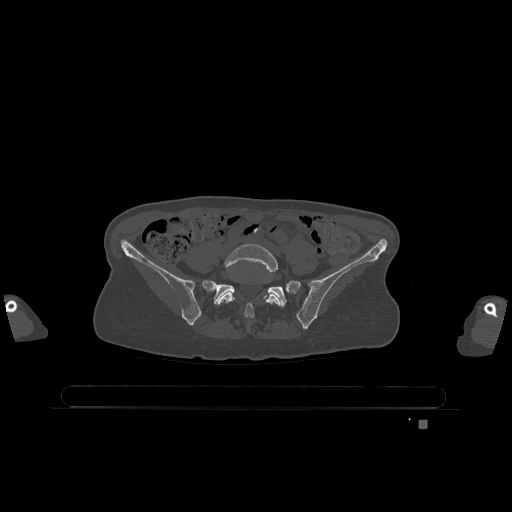
CT including the spine, one axial slice; slice 218 of 1317 in the series (ordered by position); bone window (W 1800 / L 400 HU); 512 × 512 image matrix, field of view 500 × 500 mm. Patient: female, 74 years. From the clinical record (not read from this slice): primary cancer: lung; vertebrae with lytic lesions (as recorded): T1, T4, T5, T6, L4, L5.
Outlined on this slice (semi-automatic segmentation, software-assisted and operator-edited):
- L5 vertebra: bounding box [x1, y1, x2, y2] px = [217, 244, 281, 318]